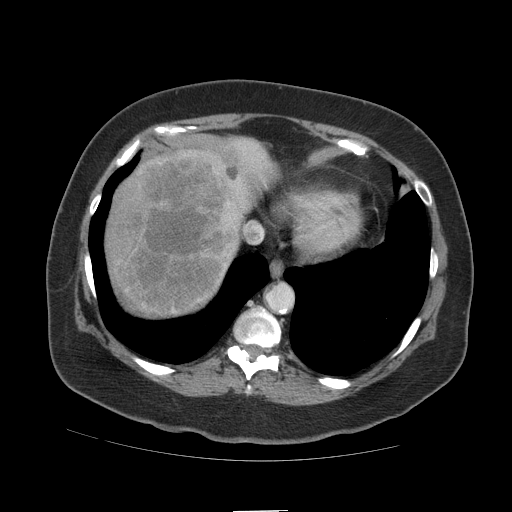
Contrast-enhanced abdominal CT (liver protocol), one axial slice; position 93 of 109 along the scan axis; 140 kVp; soft-tissue window (W 400 / L 40 HU); 512 × 512 image matrix. Case-level facts recorded for this patient, not image findings: diagnosis: hepatocellular carcinoma (patient treated with transarterial chemoembolisation; whether this scan precedes or follows treatment is not stated here); TNM stage (as recorded): Stage-IVB; Child-Pugh class: A.
Outlined on this slice (semi-automatically segmented with operator editing):
- liver parenchyma outside the tumour (the mass and vessels are separate outlines, so this box may not span the whole liver): bounding box (x1, y1, x2, y2) in pixels: (104, 136, 276, 316)
- mass: (105, 147, 243, 314)